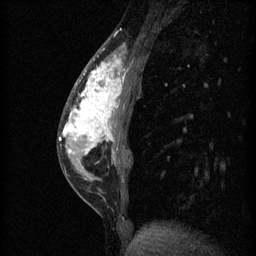
Breast MRI (dynamic contrast-enhanced), one sagittal slice; position 20 of 60 along the scan axis; 3 images stored at this slice position (order not interpretable as contrast timing); 1.5 T; TE 4.2 ms, TR 11 ms; 2 mm slice thickness; 256 × 256 image matrix. Patient: female, 40 years.
Annotated regions visible in this slice (semi-automatic segmentation, software-assisted and operator-edited):
- analysis volume of interest (the breast-tissue region the enhancement analysis was run in; not a lesion): bounding box <59,42,132,203> (left, top, right, bottom; pixels)
- tumour enhancement mask (voxels above the 70 % enhancement threshold inside the analysis volume of interest): <60,56,123,155>